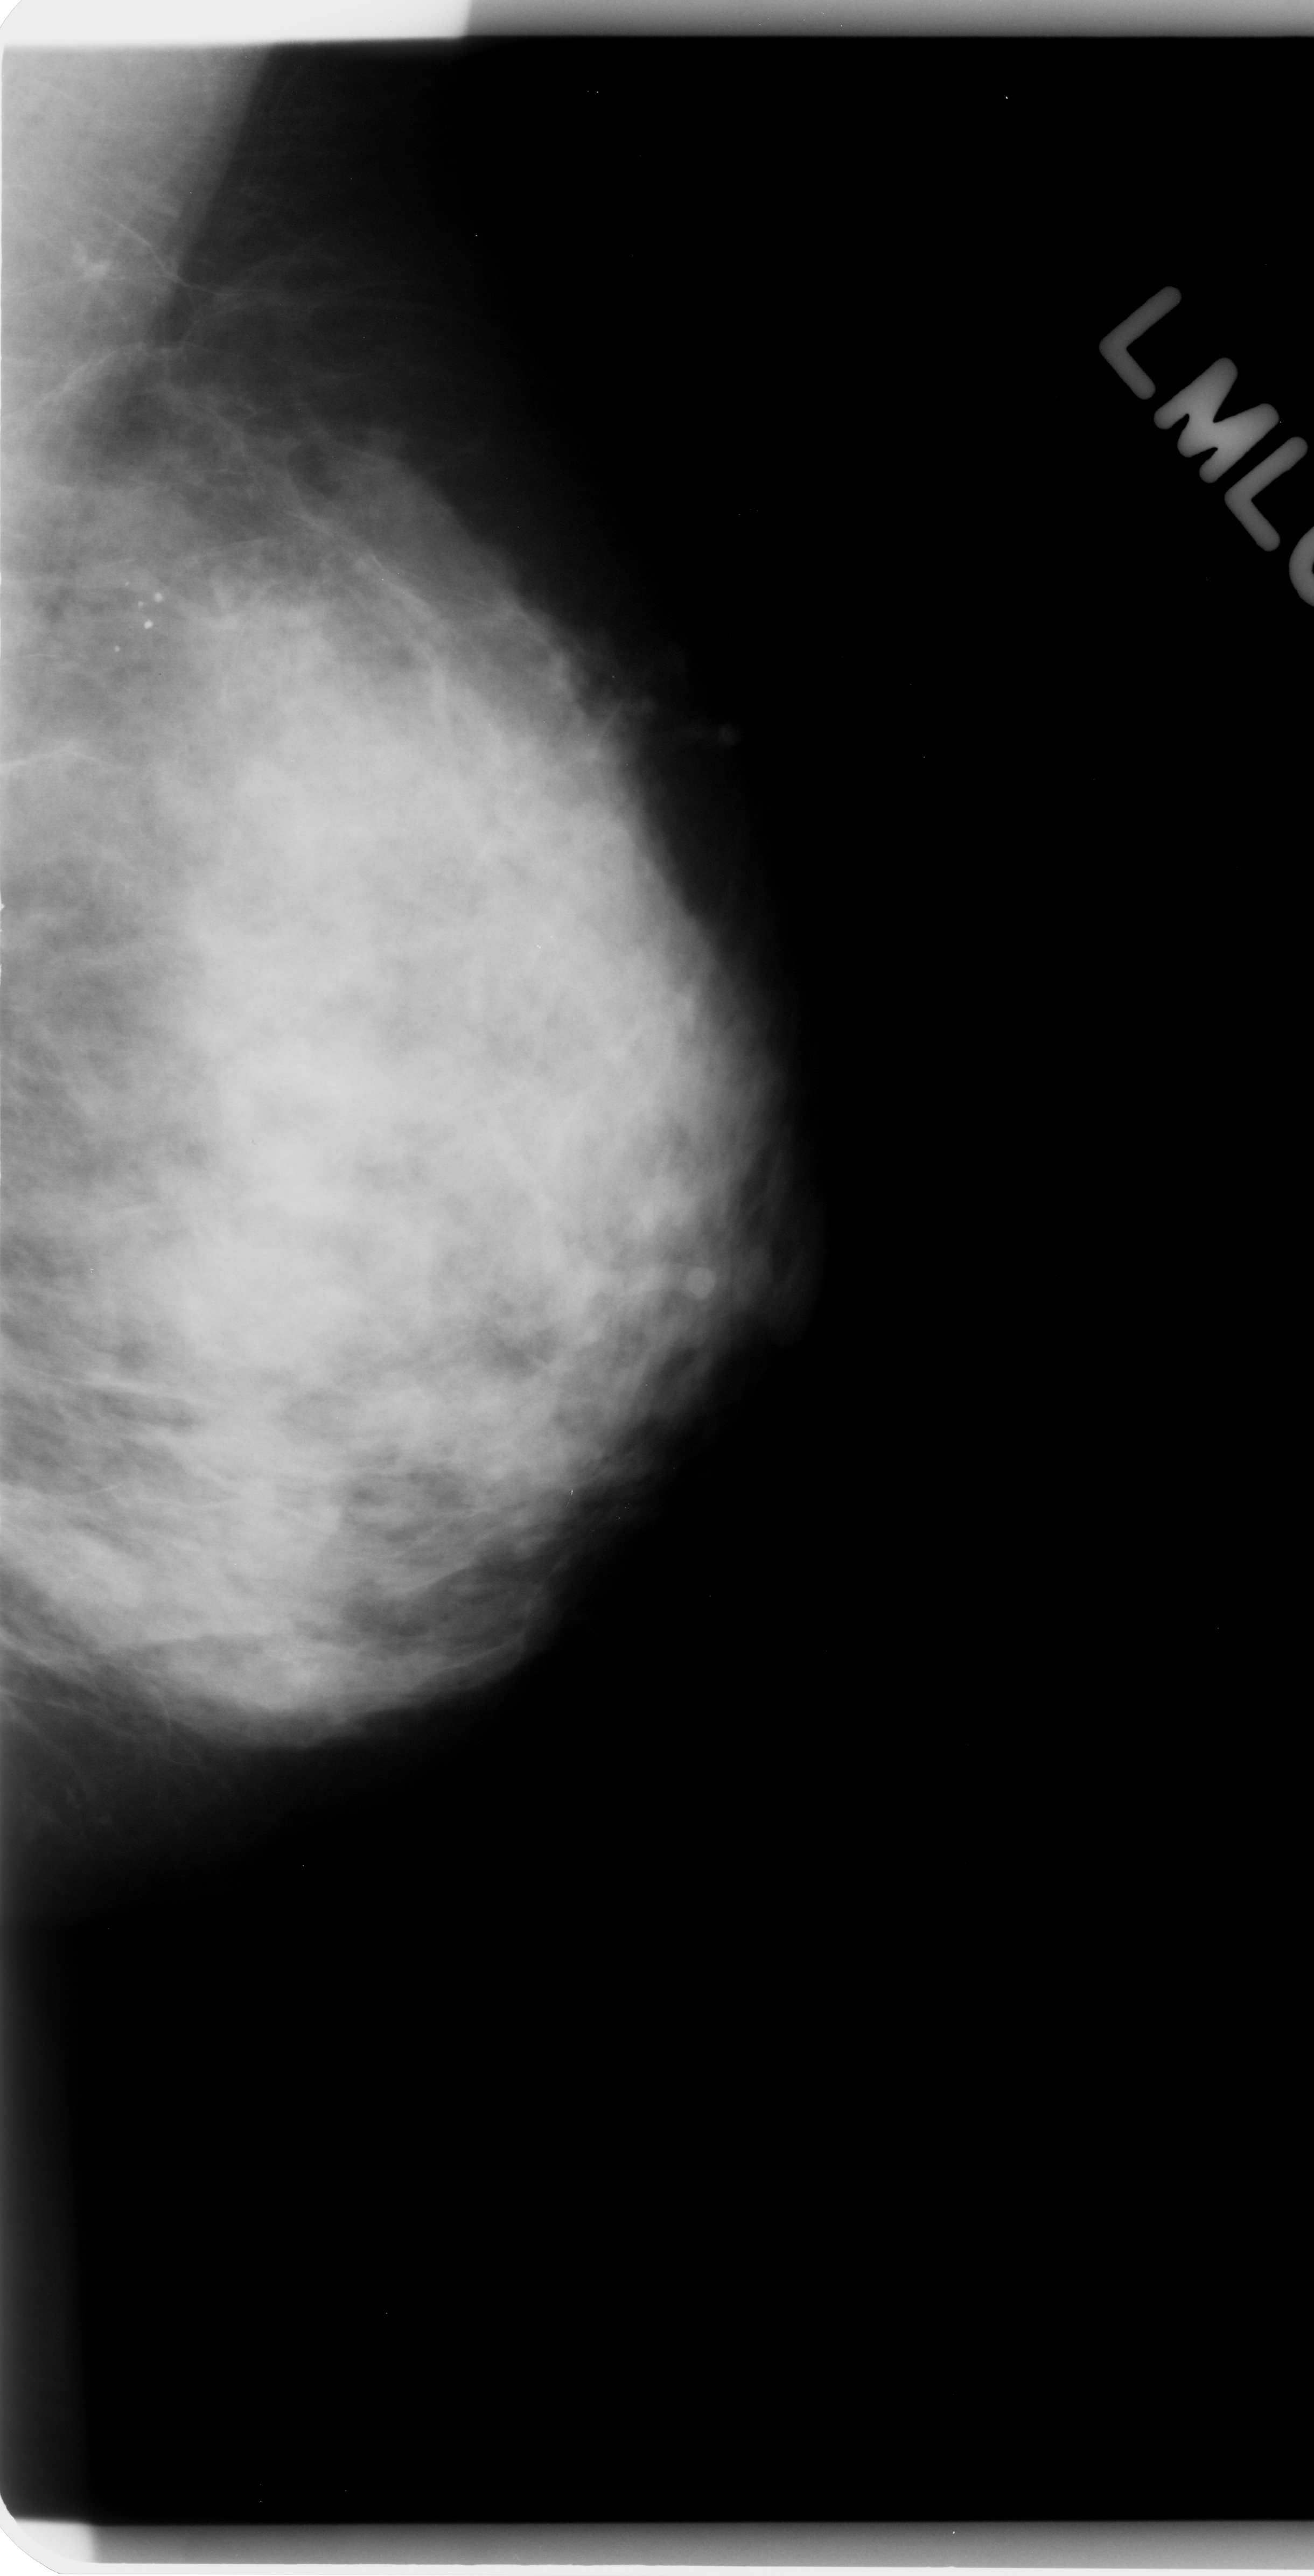
Scanned film-screen mammogram; left breast; mediolateral oblique (MLO) view; BI-RADS breast density category 3 (scale 1–4); 1314 × 2576 image matrix.
Expert-marked regions of interest on this film, with their recorded descriptors:
- calcifications, morphology pleomorphic, distribution clustered; BI-RADS assessment category 4; subtlety rating 5 on a 1 (subtle) to 5 (obvious) scale; pathology result (as recorded, not read from the image): benign: box from (x=77, y=521) to (x=199, y=725) px